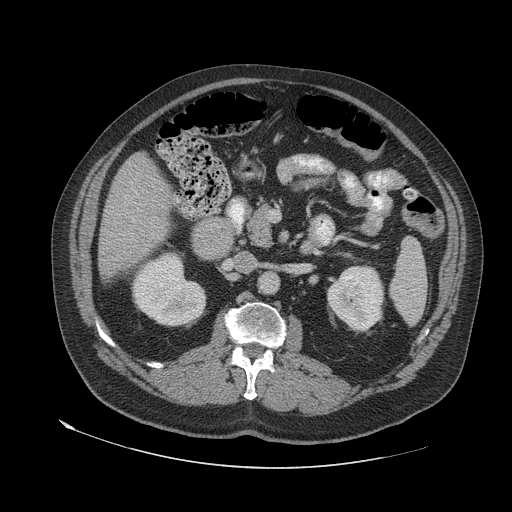
Contrast-enhanced abdominal CT (liver protocol), one axial slice; position 21 of 79 along the scan axis; reconstruction kernel STANDARD; 140 kVp; soft-tissue window (W 400 / L 40 HU); 512 × 512 image matrix, field of view 480 × 480 mm. From the clinical record (not read from this slice): diagnosis: hepatocellular carcinoma (patient treated with transarterial chemoembolisation; whether this scan precedes or follows treatment is not stated here); TNM stage (as recorded): Stage-IVA; Child-Pugh class: A.
Annotated regions visible in this slice (semi-automatically segmented with operator editing):
- liver parenchyma outside the tumour (the mass and vessels are separate outlines, so this box may not span the whole liver): box from (x=98, y=152) to (x=172, y=280) px